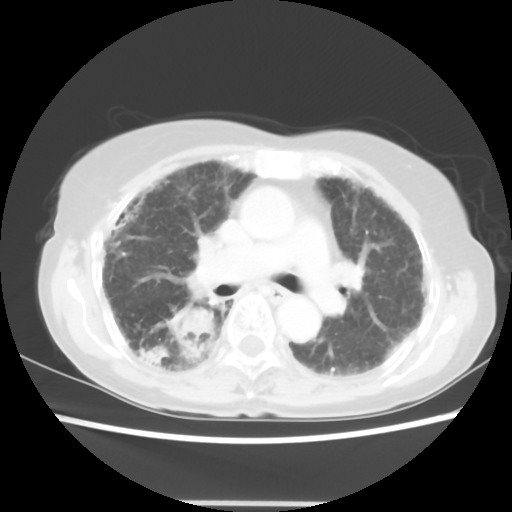
Chest CT, one axial slice. Slice 32 of 52 in the series (ordered by position). Lung window (W 1500 / L -600 HU). 5 mm slice thickness. 512 × 512 image matrix. Female patient, age 71 years. Case-level facts recorded for this patient, not image findings: clinical TNM (as recorded): T3 N0 M0.
Structures marked on this image (bounding box drawn by a radiologist):
- lung tumour (recorded histology: squamous cell carcinoma): box from (x=163, y=305) to (x=211, y=359) px